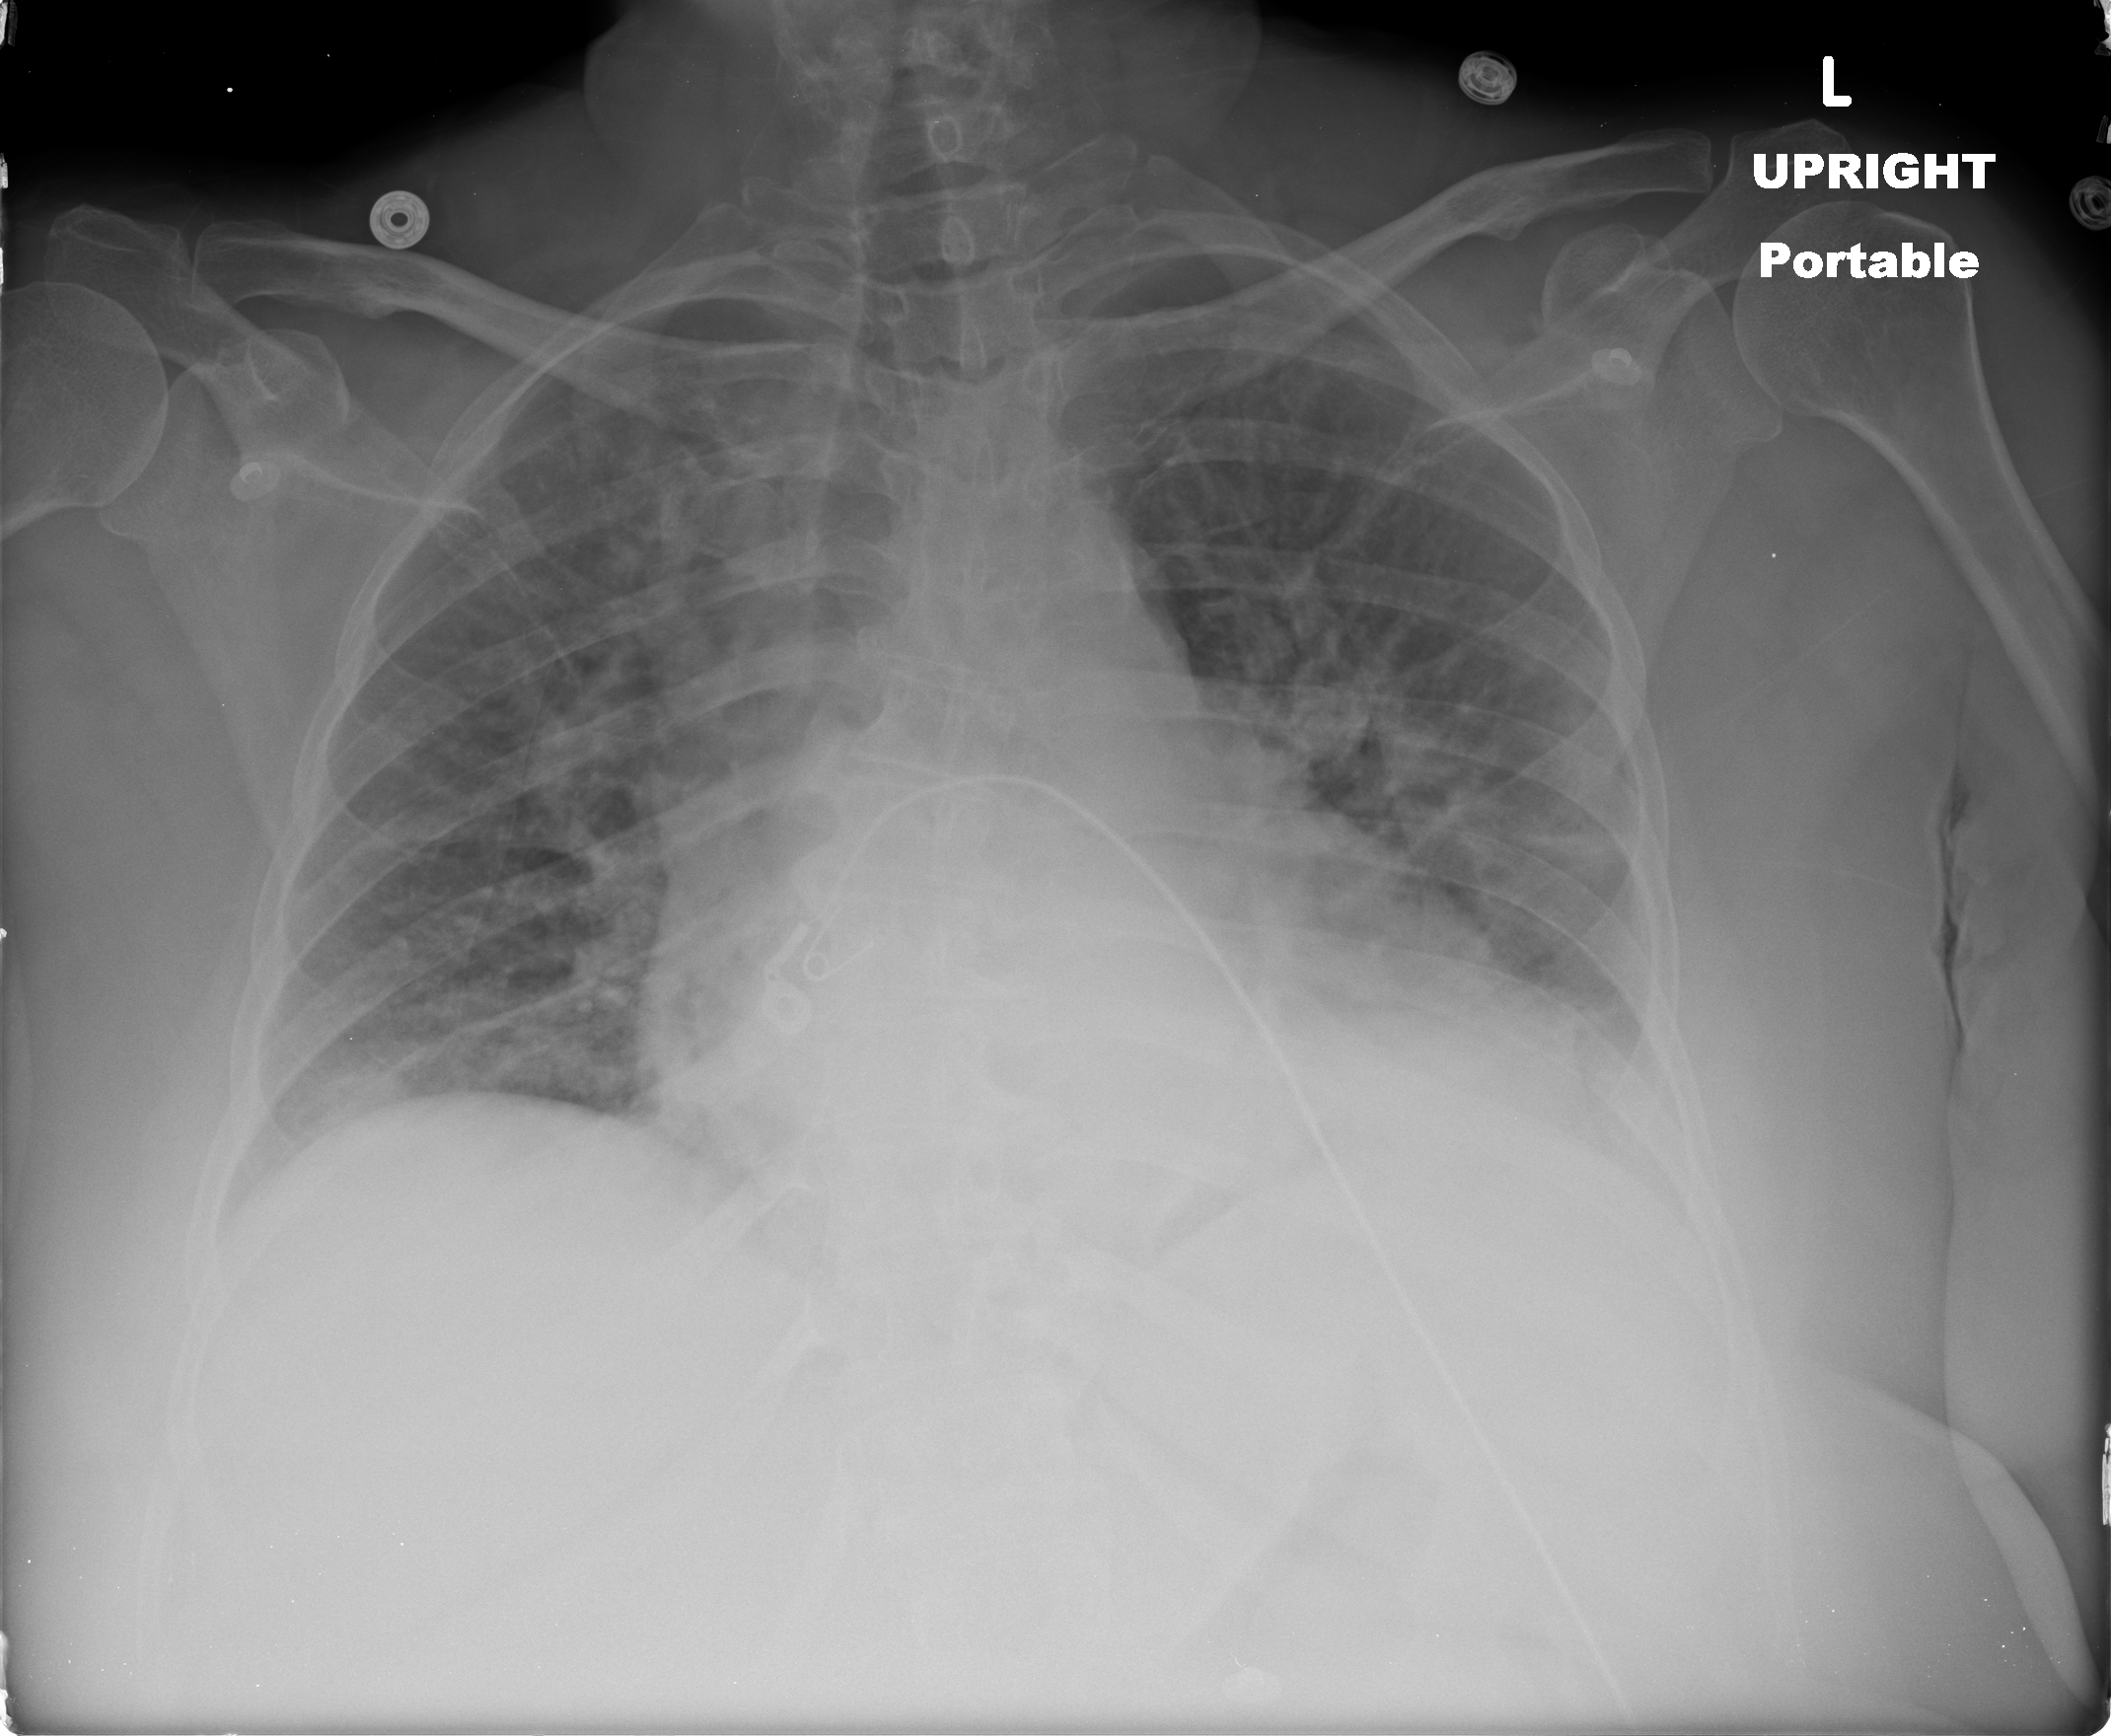
Chest X-ray (portable), AP projection. Female patient, age 50 years; imaged 2 days after the COVID-19 diagnosis.
Key findings recorded by the radiologist: Slightly increased consolidation in the left lower lobe. Few scattered patchy airspace opacities and linear atelectatic changes in both lungs, grossly unchanged.